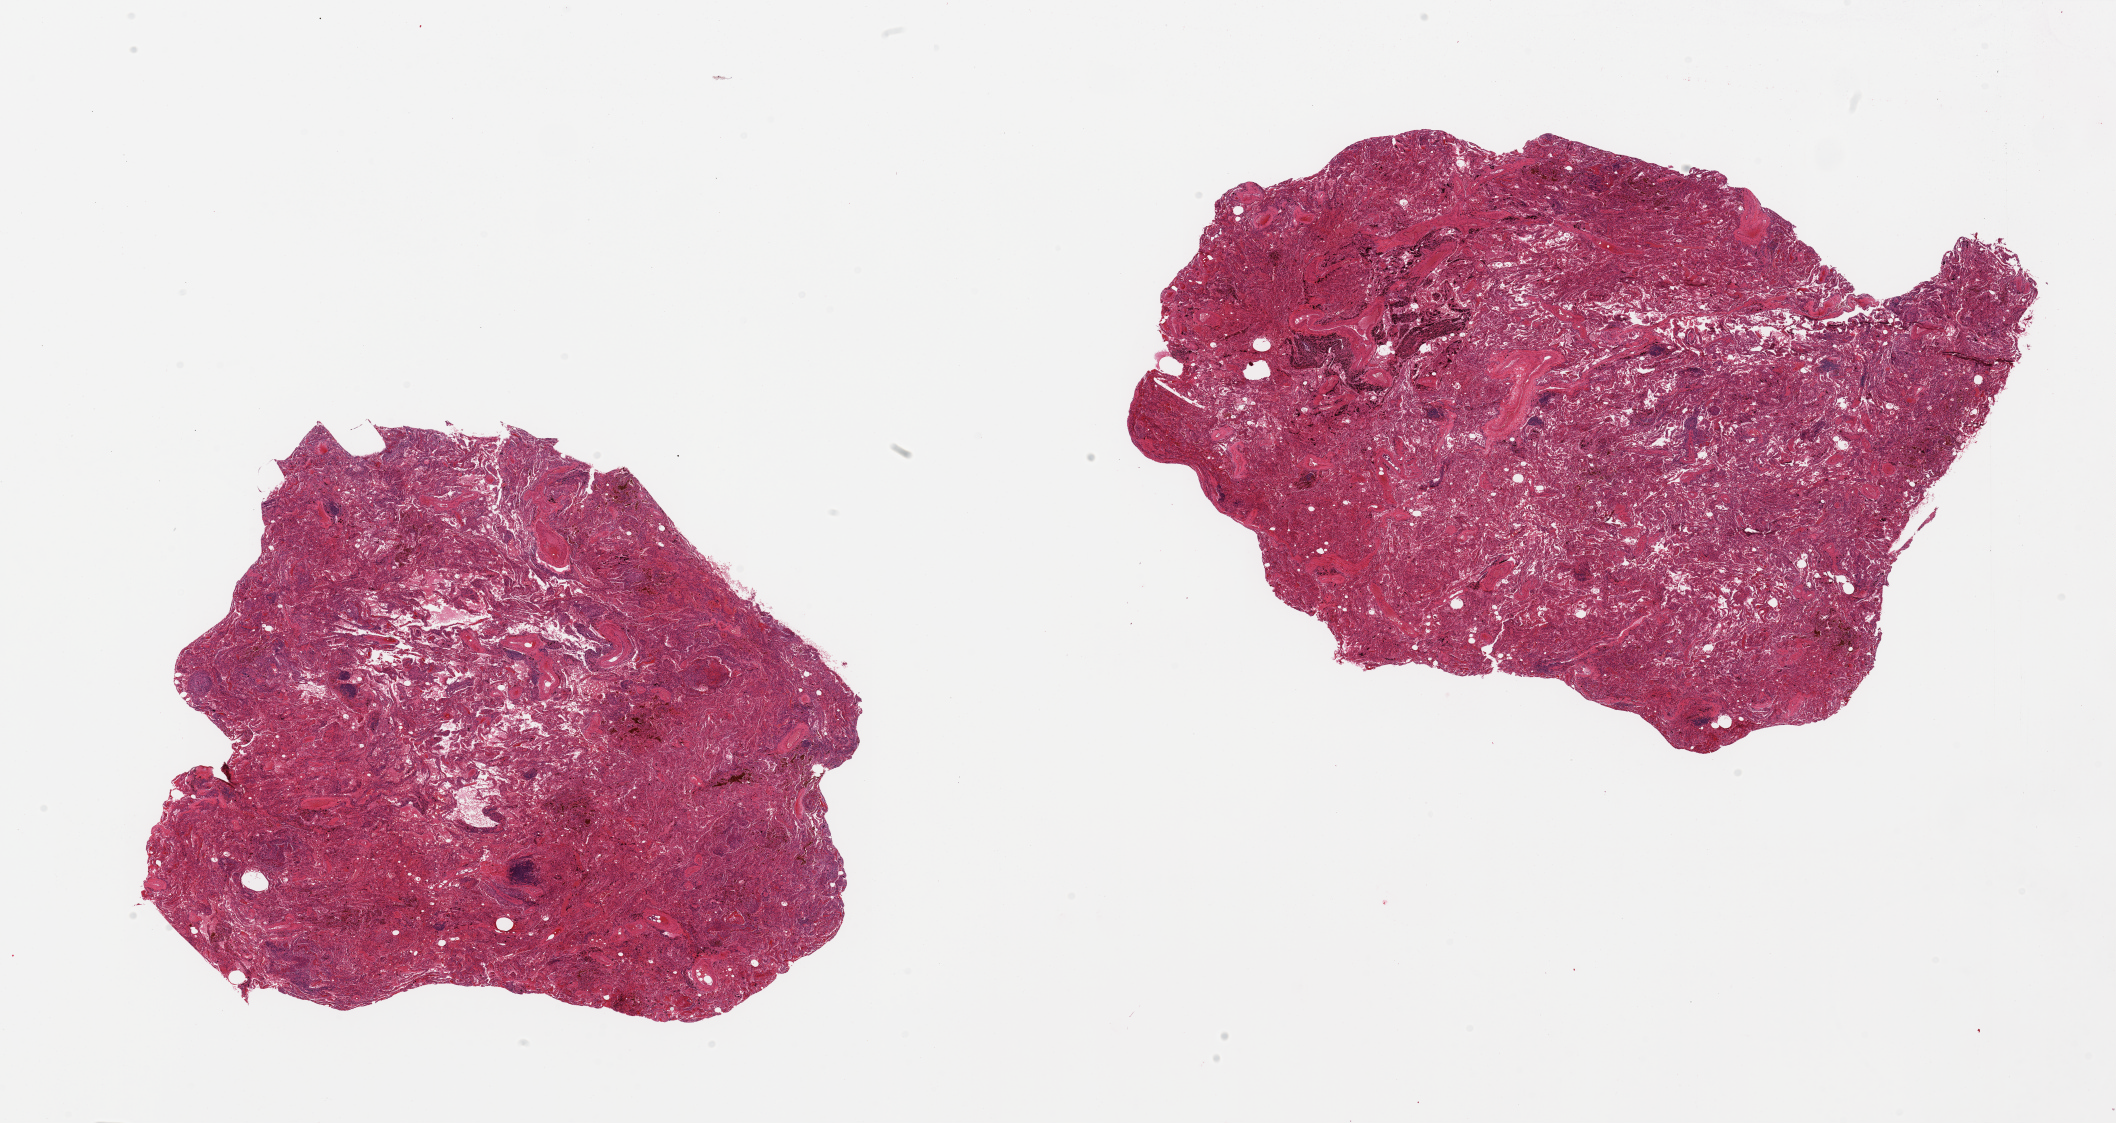
Digitized haematoxylin and eosin-stained section, shown as a low-resolution overview of the whole scanned area (about 33.5 x 17.8 mm). PAXgene-fixed paraffin-embedded (PFPE) section. Section of lung (target tissue). Donor tissue sample. Male donor.
* reviewer comment on this tissue sample: 2 pieces; diffuse interstitial fibrosis with granulomatous and chronic inflammation, abundant pigmented macrophages